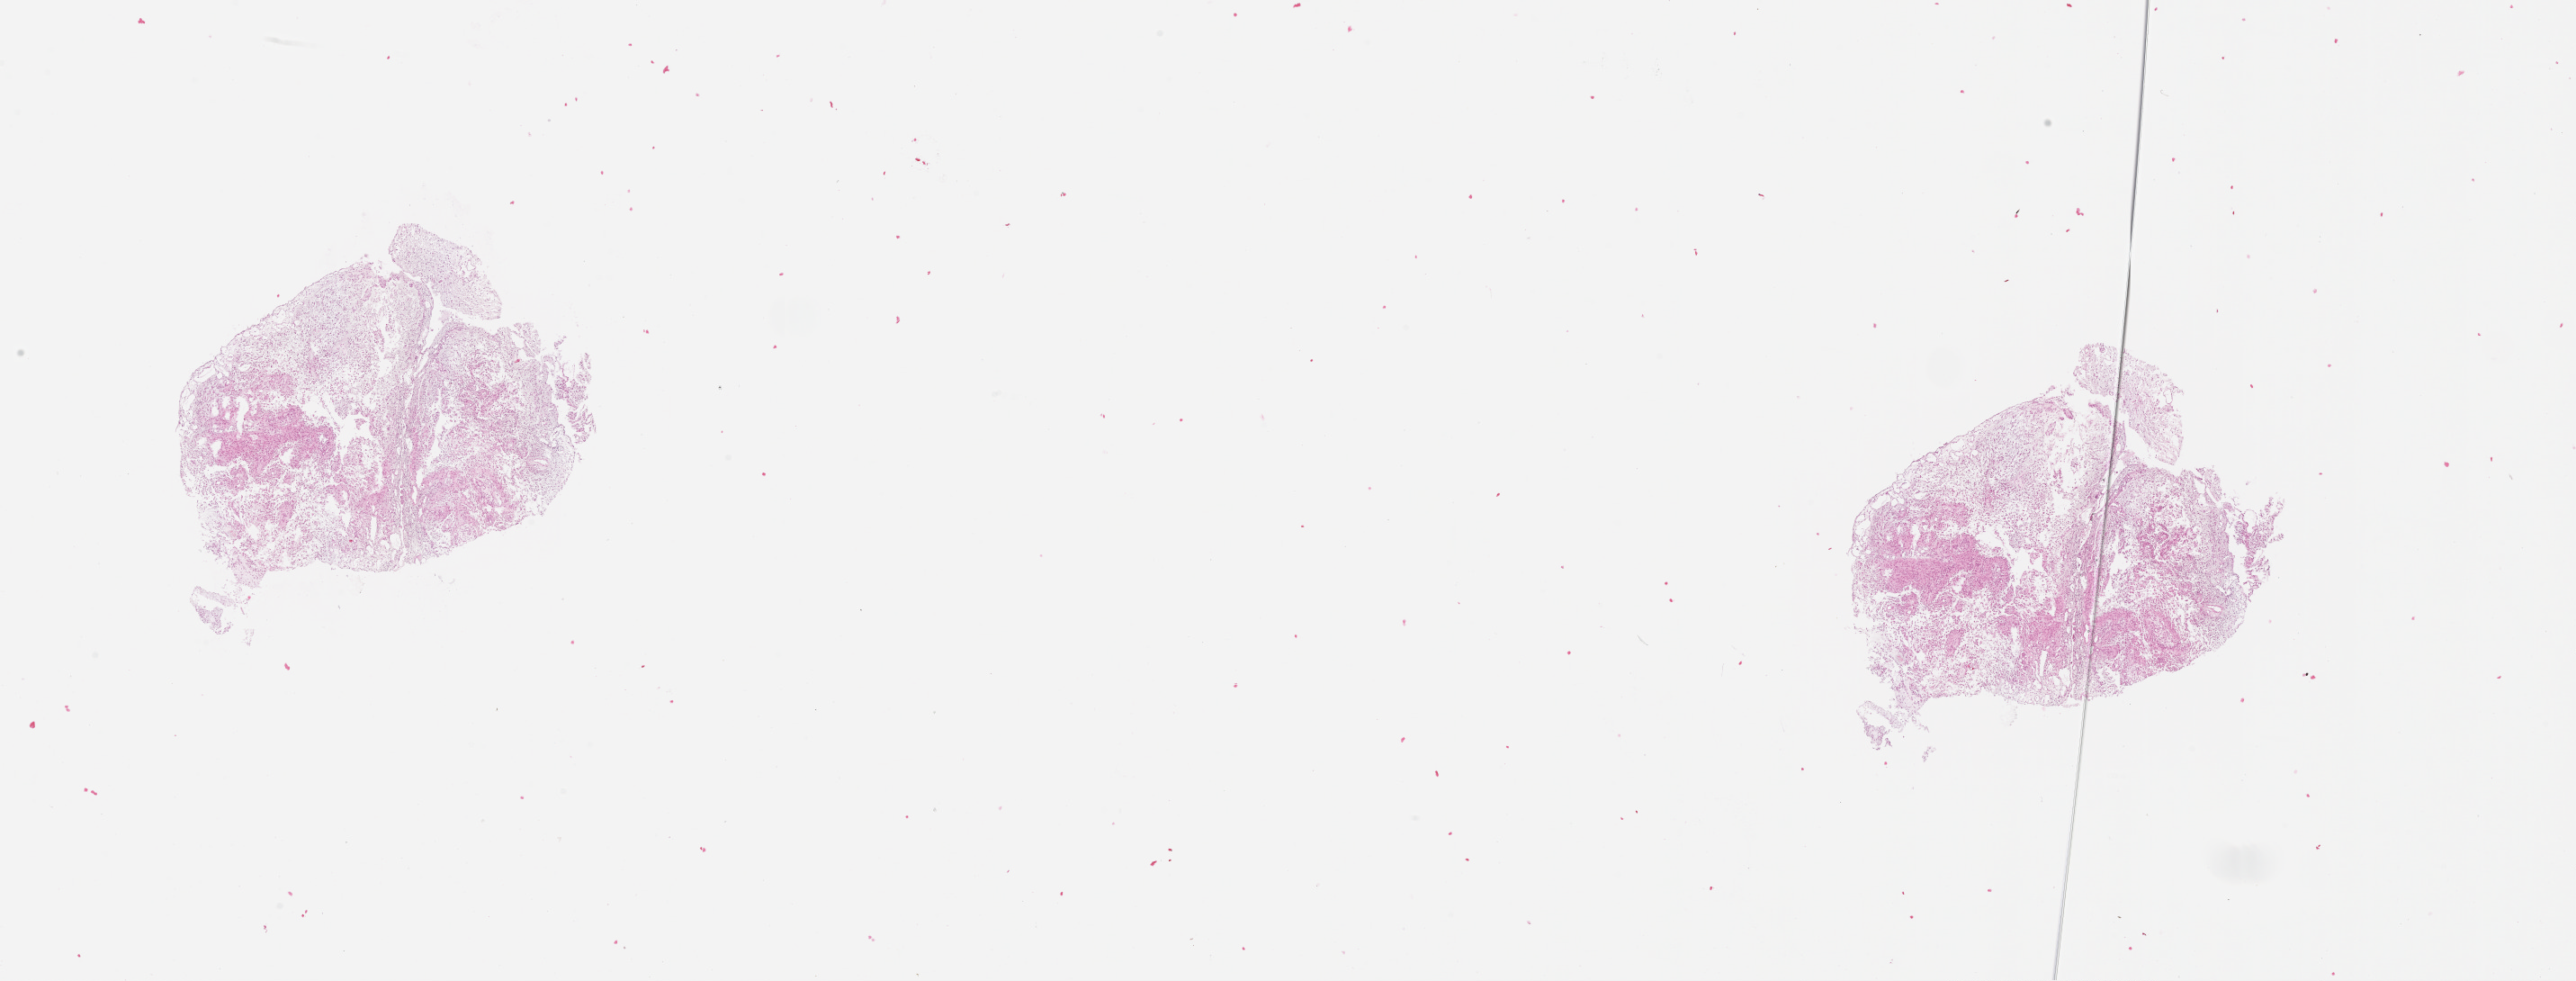
Digitized Hematoxylin and eosin (H&E) stained tissue section (whole slide) — shown as a low-resolution overview of the whole scanned area (about 23.1 x 8.8 mm); tumour tissue sample, sampled site: brain. Male, 68 y/o. Composition of this section per pathologist review: tumour nuclei 70%, necrosis 10%.
* primary tumour site (as recorded): temporal lobe
* diagnosis: Glioblastoma